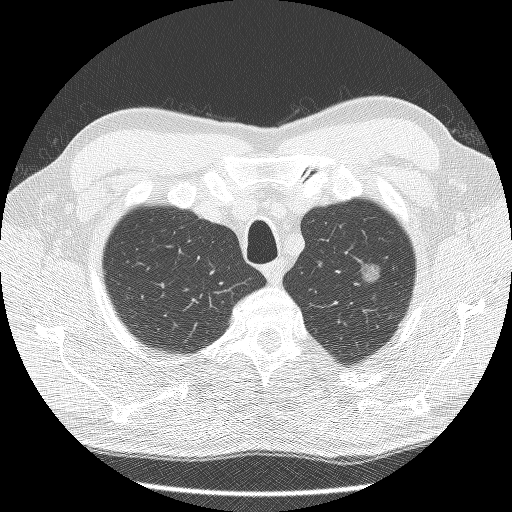
Axial slice from a low-dose chest CT screening exam; third screening round (two years after baseline); lung window (W 1500 / L -600 HU); lung (sharp) reconstruction kernel (BONE). Male participant, aged 60 years at enrolment. Former smoker at enrolment.
Lesion marked by an expert reader, bounding box (x1, y1, x2, y2) in pixels: (336, 252, 393, 300). The screening reader recorded 2 non-calcified nodules or masses ≥4 mm on this exam (right lower lobe, left upper lobe); which of them this box marks is not recorded. Later outcome: lung cancer diagnosed 99 days after this screen — bronchiolo-alveolar carcinoma, non-mucinous, left upper lobe, well differentiated (G1), stage IA (AJCC 6th edition), 16 mm at pathology.